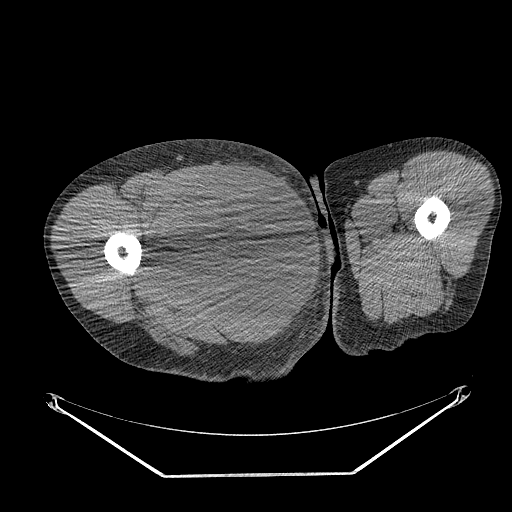
CT of an extremity soft-tissue mass (from a PET/CT study), one axial slice. Reconstruction kernel STANDARD. 140 kVp. Soft-tissue window (W 400 / L 40 HU). 3.75 mm slice thickness. 512 × 512 image matrix, field of view 500 × 500 mm. Male patient. From the clinical record (not read from this slice): histological type: undifferentiated - pleiomorphic; grade: high; site of the primary tumour: right thigh.
Annotated regions visible in this slice (expert contour drawn on MRI and transferred to this co-registered scan by the dataset authors):
- gross tumour volume including surrounding oedema: bounding box [x1, y1, x2, y2] px = [153, 169, 268, 280]
- gross tumour volume (mass): [157, 169, 268, 279]